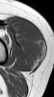
MRI of an extremity soft-tissue mass, one axial slice; position 30 of 42 along the scan axis; MR volume resampled by the dataset authors to the PET/CT grid (not the native acquisition matrix); 54 × 97 image matrix, field of view 53 × 95 mm. Female patient. Case-level facts recorded for this patient, not image findings: histological type: spindle cell suggestive of biphasic synovial sarcoma; grade: intermediate; site of the primary tumour: left knee.
Structures marked on this image (expert contour drawn on MRI and transferred to this co-registered scan by the dataset authors):
- gross tumour volume including surrounding oedema: bounding box <23,25,45,61> (left, top, right, bottom; pixels)
- gross tumour volume (mass): <23,25,45,61>